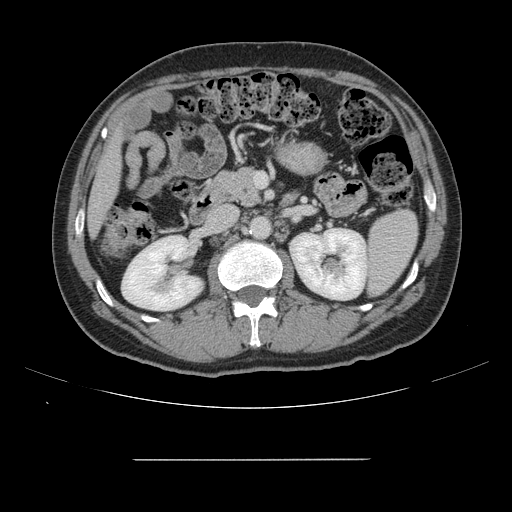
Contrast-enhanced abdominal CT, one axial slice; slice 61 of 164 in the series (ordered by position); intravenous contrast given; soft-tissue window (W 400 / L 40 HU); 2.5 mm slice thickness; 512 × 512 image matrix, field of view 404 × 404 mm. Male patient, age 54 years. From the clinical record (not read from this slice): diagnosis: colorectal cancer liver metastases, imaged before liver resection; multiple liver metastases: yes; largest metastasis: 1 cm.
Outlined on this slice (manually delineated by an expert):
- liver: box from (x=89, y=133) to (x=121, y=233) px
- planned liver remnant (the part of the liver to remain after resection): (x=89, y=136)–(x=120, y=232)